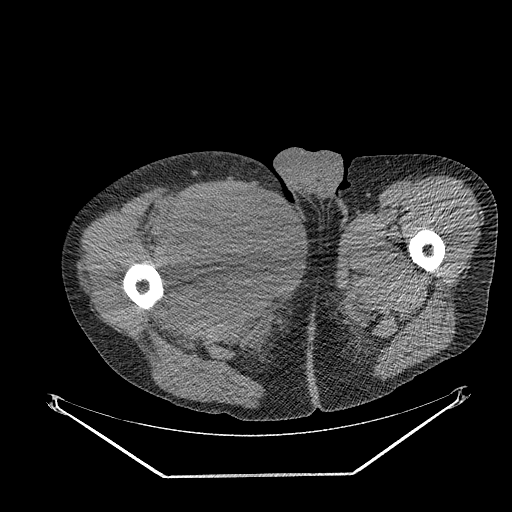
CT of an extremity soft-tissue mass (from a PET/CT study), one axial slice; position 279 of 311 along the scan axis; reconstruction kernel STANDARD; soft-tissue window (W 400 / L 40 HU); 3.75 mm slice thickness; 512 × 512 image matrix, field of view 500 × 500 mm. Male patient. Case-level facts recorded for this patient, not image findings: histological type: undifferentiated - pleiomorphic; grade: high; site of the primary tumour: right thigh.
Outlined on this slice (expert contour drawn on MRI and transferred to this co-registered scan by the dataset authors):
- gross tumour volume including surrounding oedema: bounding box <173,185,263,277> (left, top, right, bottom; pixels)
- gross tumour volume (mass): <173,189,261,277>